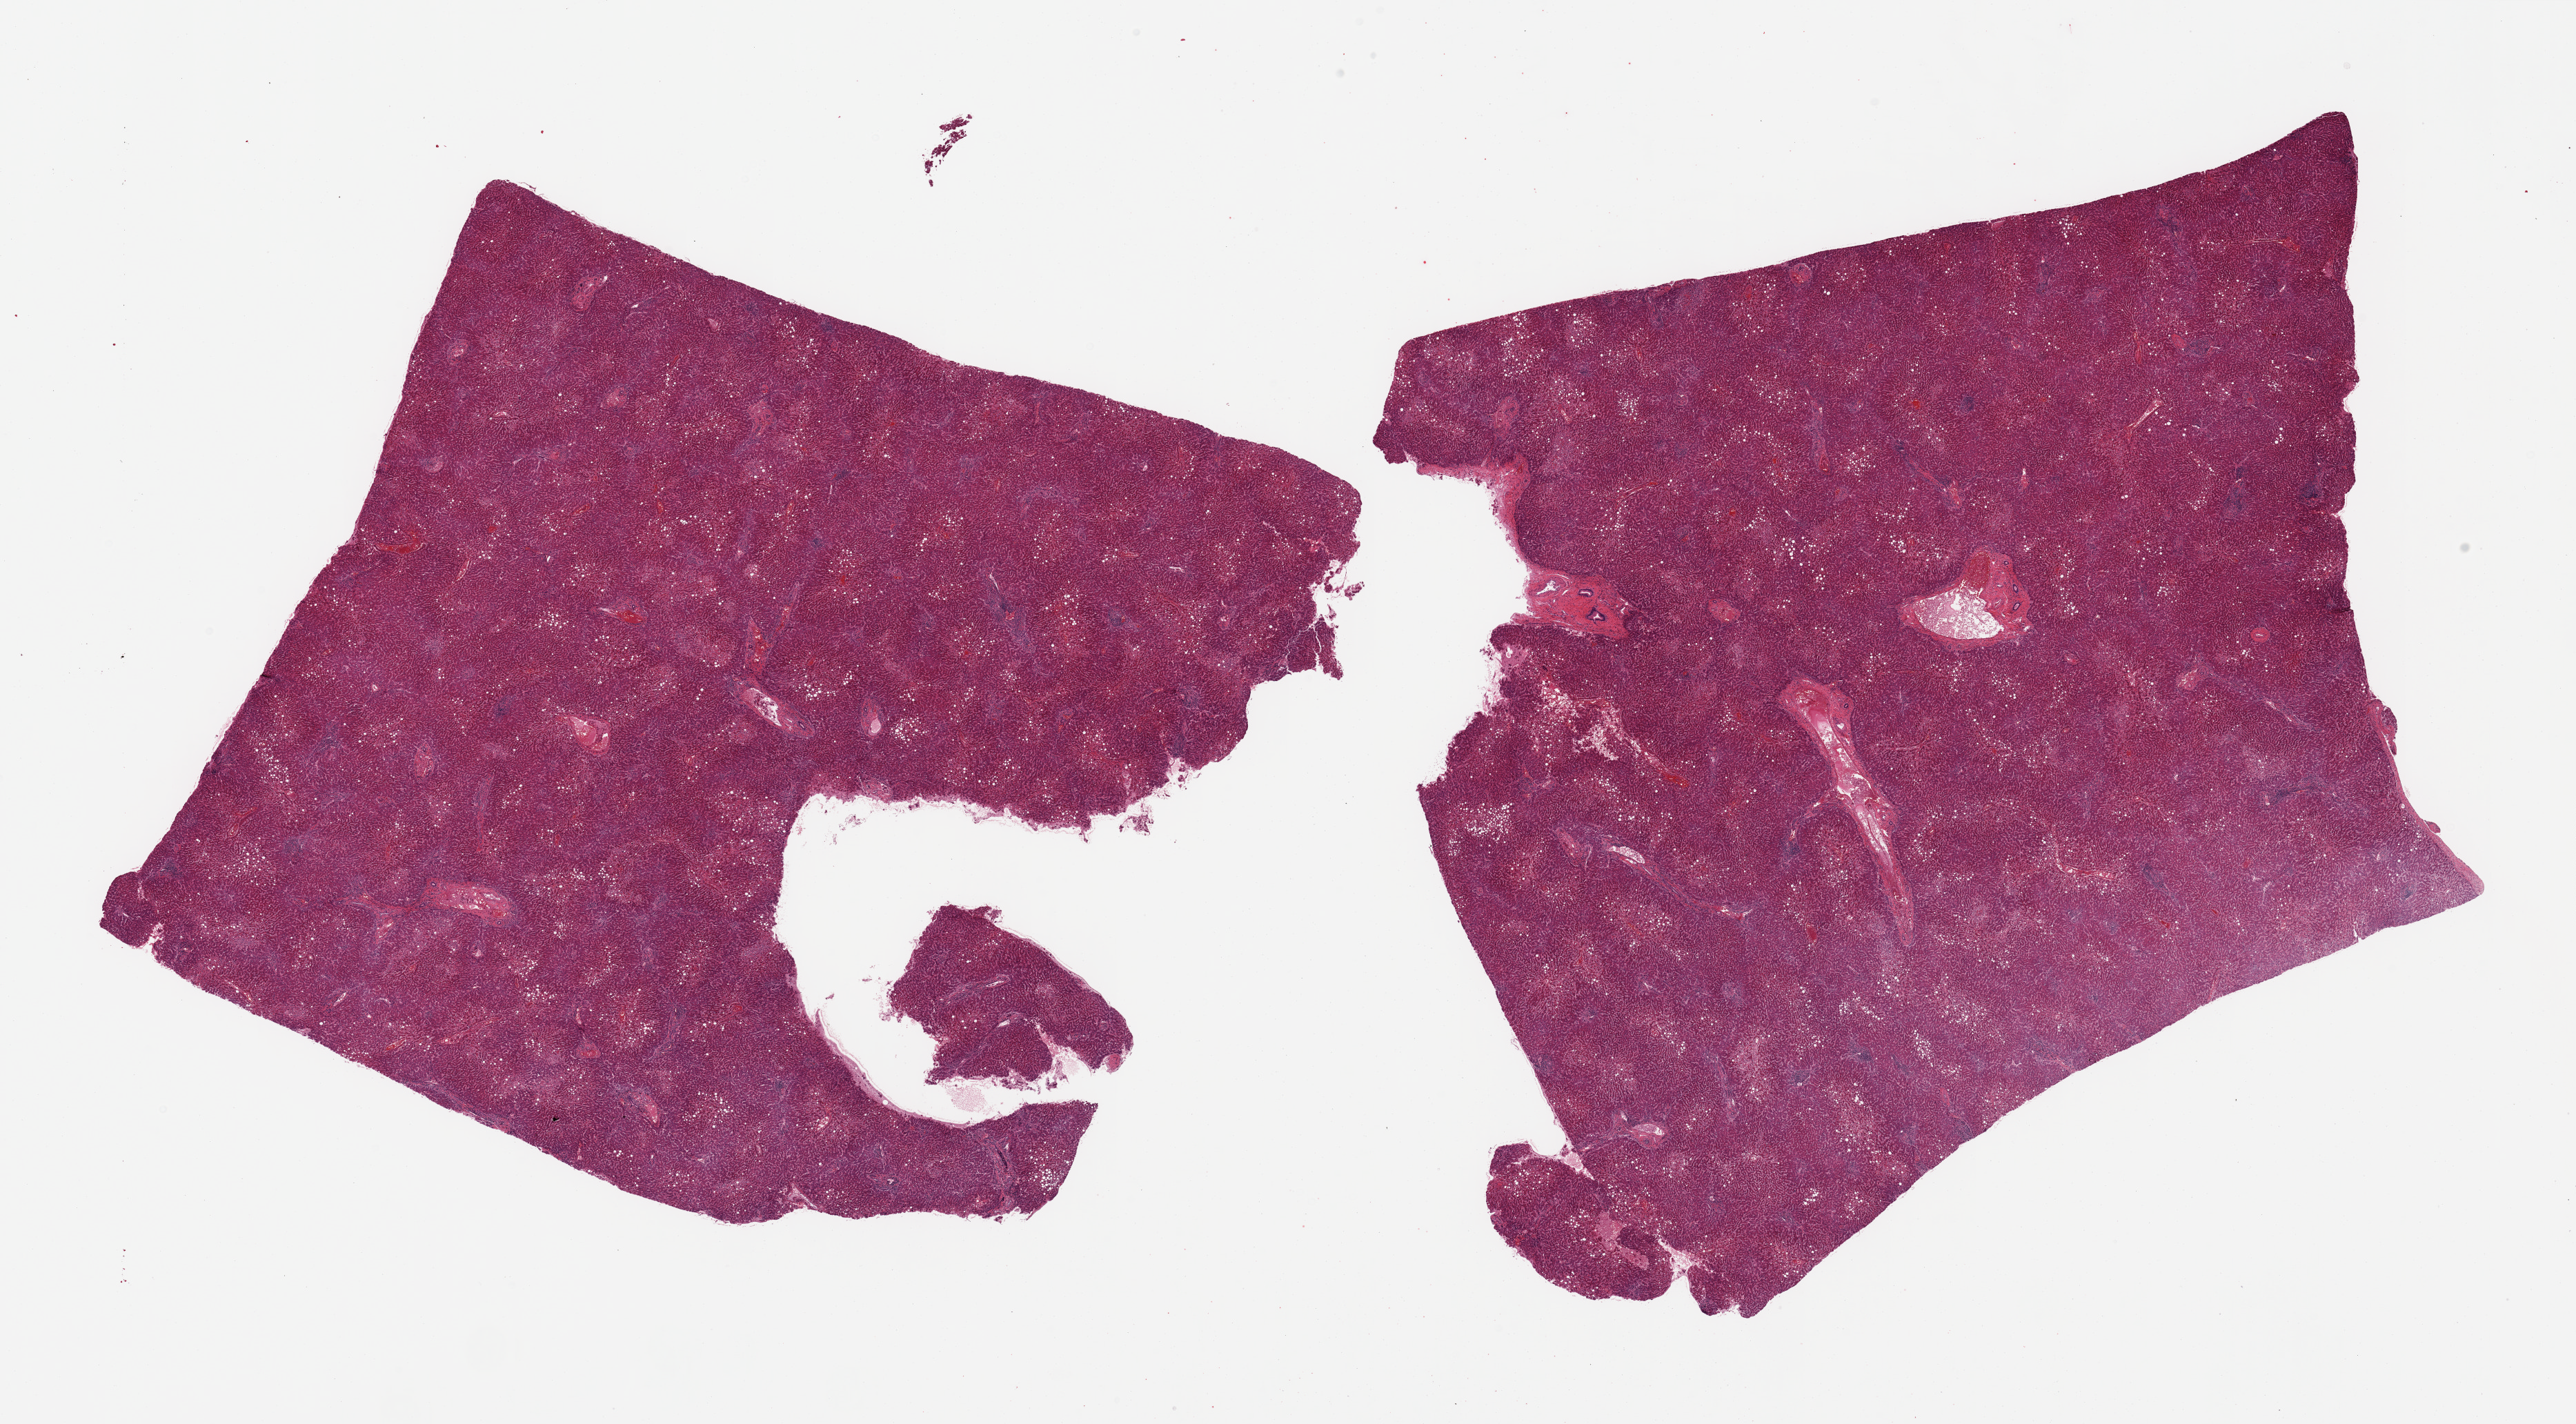
H&E whole-slide image, low-resolution overview of the scanned area, about 29.5 x 16.3 mm, PAXgene-fixed paraffin-embedded (PFPE) section, target tissue: liver, tissue donor sample. Male donor.
Pathologist's review note for this sample: 2 pieces; includes portion of capsule (target is 1 cm below capsule), portal chronic inflammation, mild steatosis, centrally congested and mildly autolyzed.